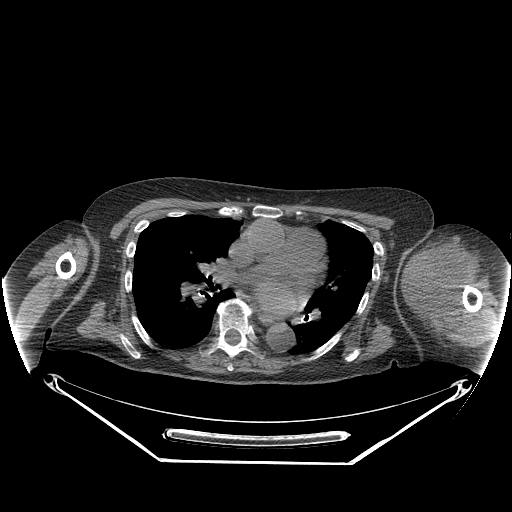
CT of an extremity soft-tissue mass (from a PET/CT study), one axial slice. Slice 175 of 267 in the series (ordered by position). Reconstruction kernel STANDARD. Soft-tissue window (W 400 / L 40 HU). 3.75 mm slice thickness. 512 × 512 image matrix, field of view 500 × 500 mm. Female patient. From the clinical record (not read from this slice): histological type: pleiomorphic leiomyosarcoma; grade: high; site of the primary tumour: left biceps.
Annotated regions visible in this slice (expert contour drawn on MRI and transferred to this co-registered scan by the dataset authors):
- gross tumour volume including surrounding oedema: bounding box <404,233,471,325> (left, top, right, bottom; pixels)
- gross tumour volume (mass): <404,235,467,314>